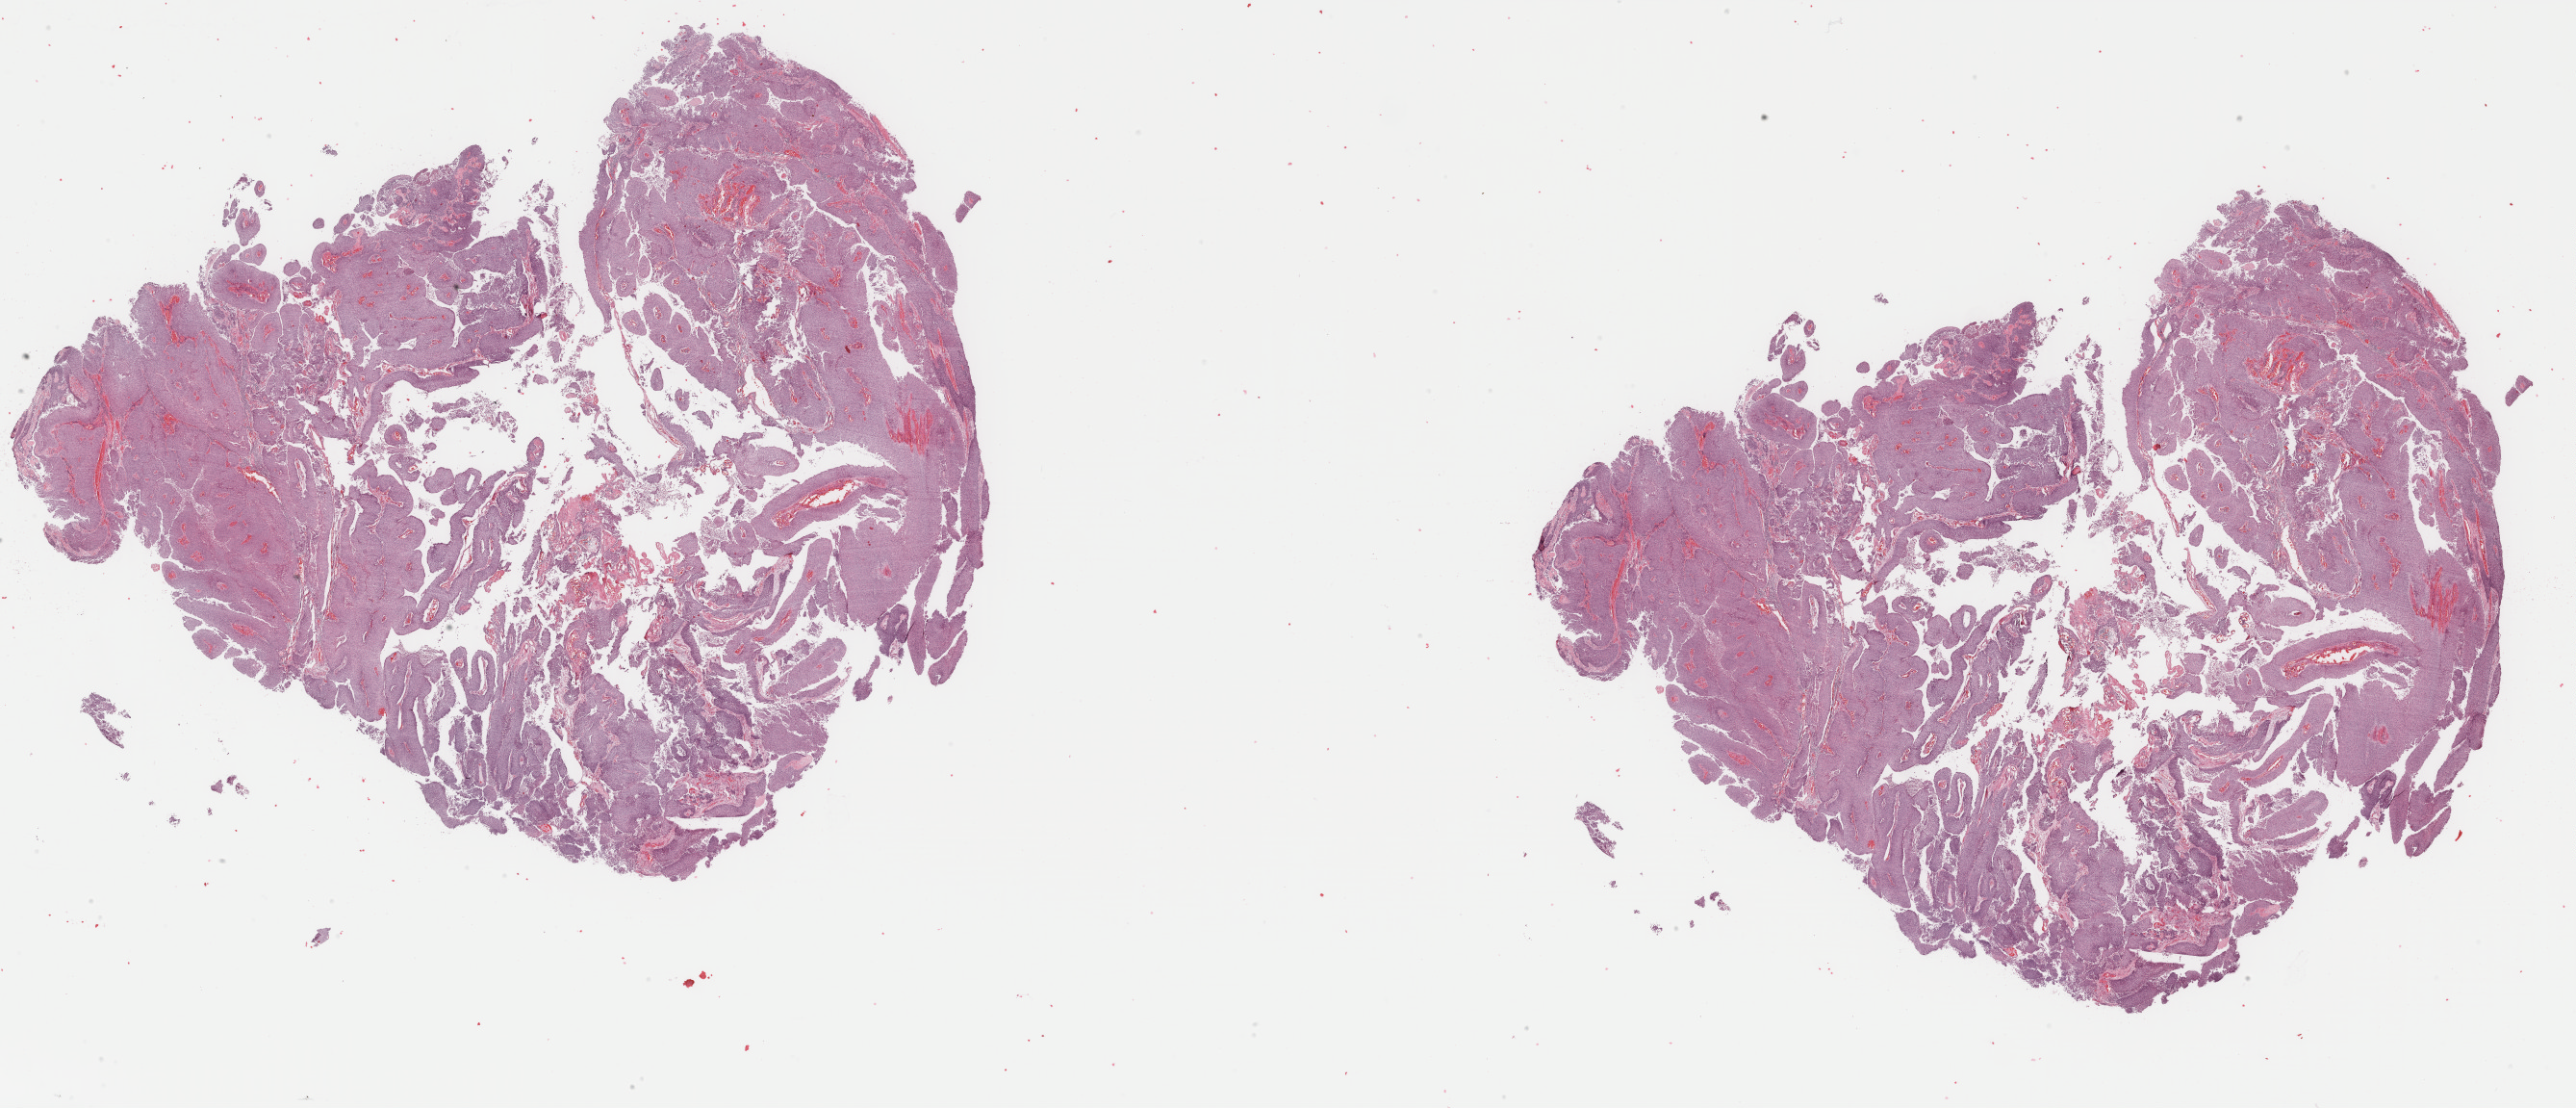
Digitized H&E tissue section (whole slide), whole scanned area (about 42.5 x 18.3 mm, from a 40x scan) shown as a low-resolution overview. Formalin-fixed paraffin-embedded (FFPE) diagnostic section. Bladder, primary tumour sample. Male, age 67 years at initial diagnosis. Histologic grade: high grade.
Lymph nodes positive (case pathology): 0 of 7 examined. Diagnosis: Papillary transitional cell carcinoma. AJCC pathologic stage: III (7th edition).